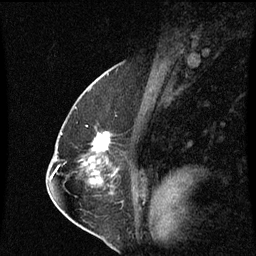
Breast MRI (dynamic contrast-enhanced), one sagittal slice; slice 38 of 60 in the series (ordered by position); dynamic contrast-enhanced series, image 2 of 3 at this slice position (ordered by acquisition); 1.5 T; TE 4.2 ms, TR 8.9 ms; 2 mm slice thickness; 256 × 256 image matrix, field of view 200 × 200 mm. Patient: female, 57 years. Case-level facts recorded for this patient, not image findings: setting: breast cancer imaged before/during neoadjuvant chemotherapy; receptor status: HR-positive, HER2-negative.
Annotated regions visible in this slice (semi-automatic segmentation, software-assisted and operator-edited):
- analysis volume of interest (the breast-tissue region the enhancement analysis was run in; not a lesion): bounding box (x1, y1, x2, y2) in pixels: (83, 128, 108, 159)
- tumour enhancement mask (voxels above the 70 % enhancement threshold inside the analysis volume of interest): (94, 134, 108, 149)